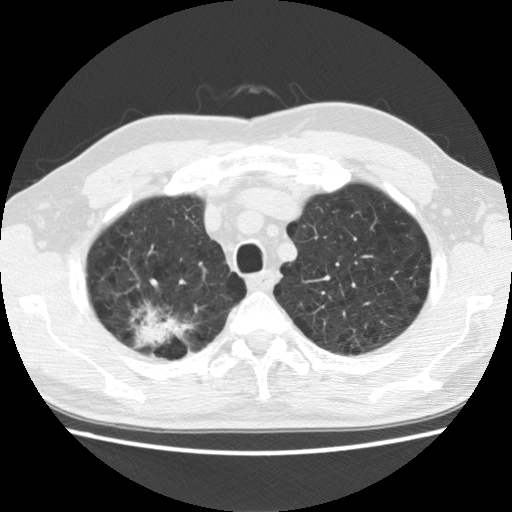
Low-dose screening chest CT, one axial slice. Position 113 of 142 along the scan axis. Lung window (W 1500 / L -600 HU). 2.5 mm slice thickness. 512 × 512 image matrix, field of view 340 × 340 mm.
Structures marked on this image (manually delineated by an expert):
- lesion 1 (tumor, upper lobe of right lung): bounding box (x1, y1, x2, y2) in pixels: (137, 320, 166, 345)